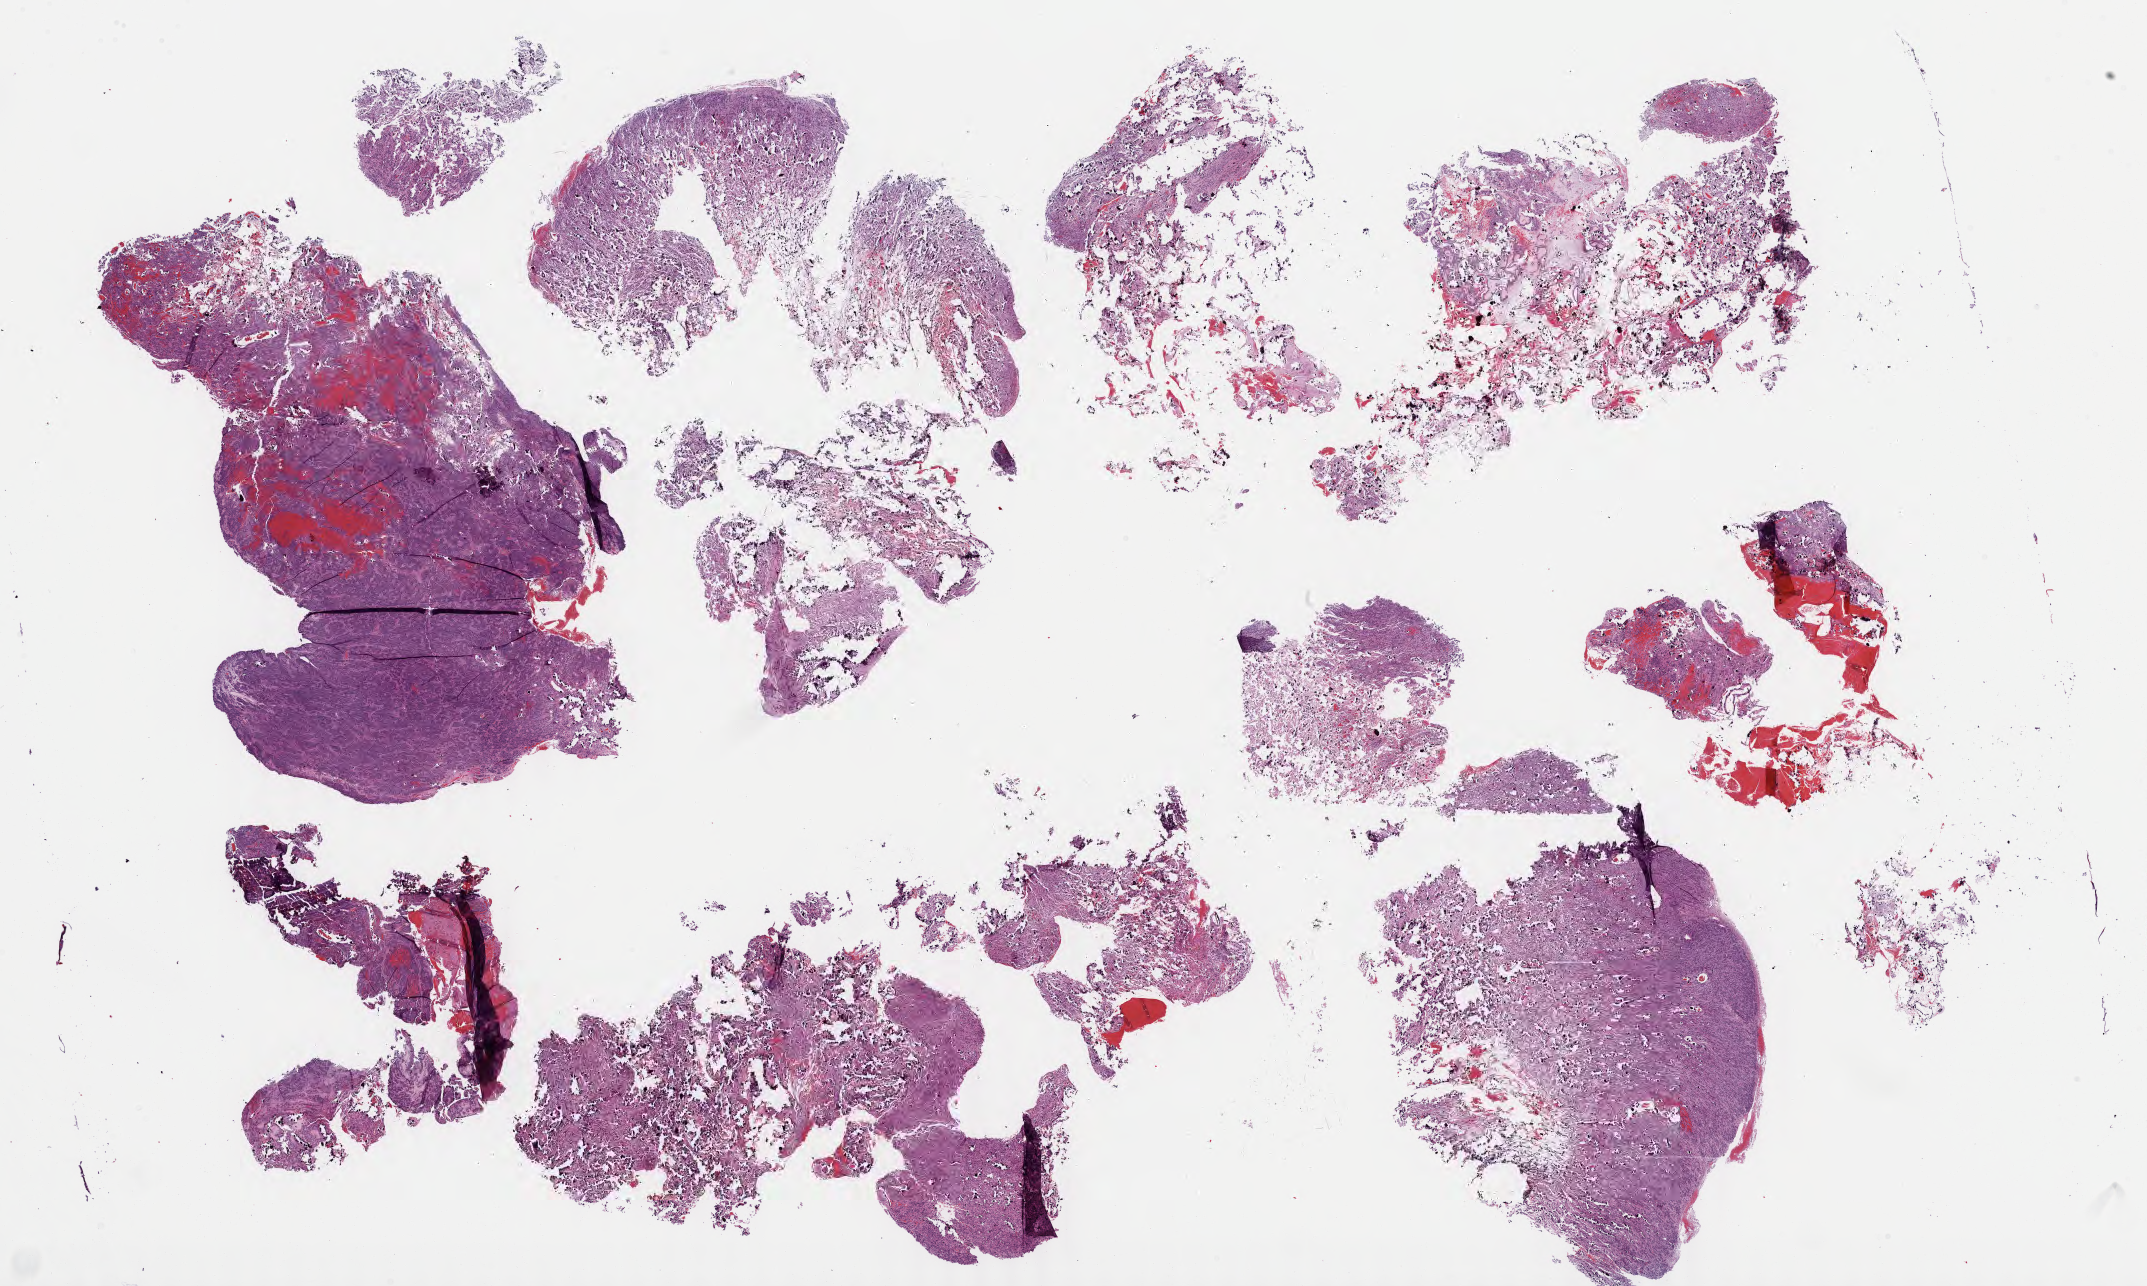
Hematoxylin and eosin (H&E) whole-slide image of tumor tissue from the parietal lobe, low-resolution overview of the scanned area, about 34.7 x 20.8 mm. Formalin-fixed paraffin-embedded section. Patient: female, age 53 months (4 years 5 months).
Diagnosis (ICD-O-3 morphology term): Atypical teratoid/rhabdoid tumor.